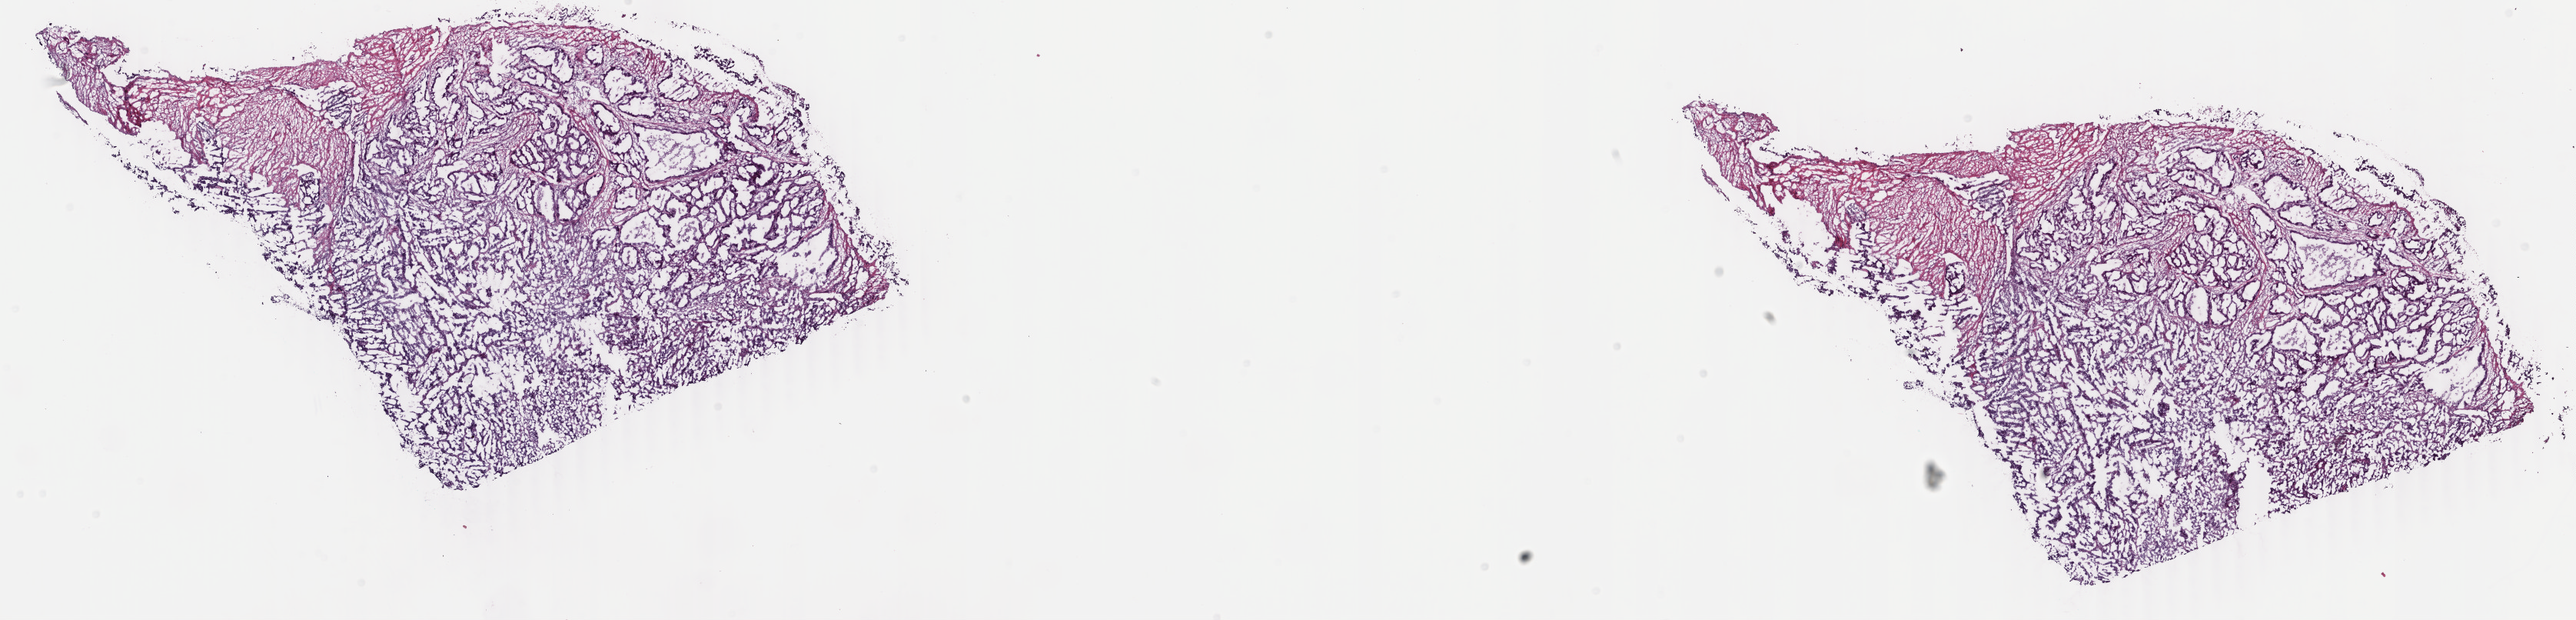
Whole-slide histology image, Hematoxylin and eosin (H&E) stained, low-resolution overview of the scanned area, about 26.7 x 6.4 mm (acquisition: 40x scan); frozen section from the top of the tissue portion; primary tumour sample from the uterus. Female patient; age at initial diagnosis 68 years. Histologic grade: G3 (poorly differentiated). Composition of this section per pathologist review: tumour cells 60%, tumour nuclei 60%, normal cells 0%, stromal cells 35%, necrosis 5%. Infiltration values recorded for this section: lymphocyte infiltration 20%, monocyte infiltration 20%, neutrophil infiltration 20%.
FIGO stage: IB. Histologic diagnosis: Endometrioid adenocarcinoma, NOS (endometrium).